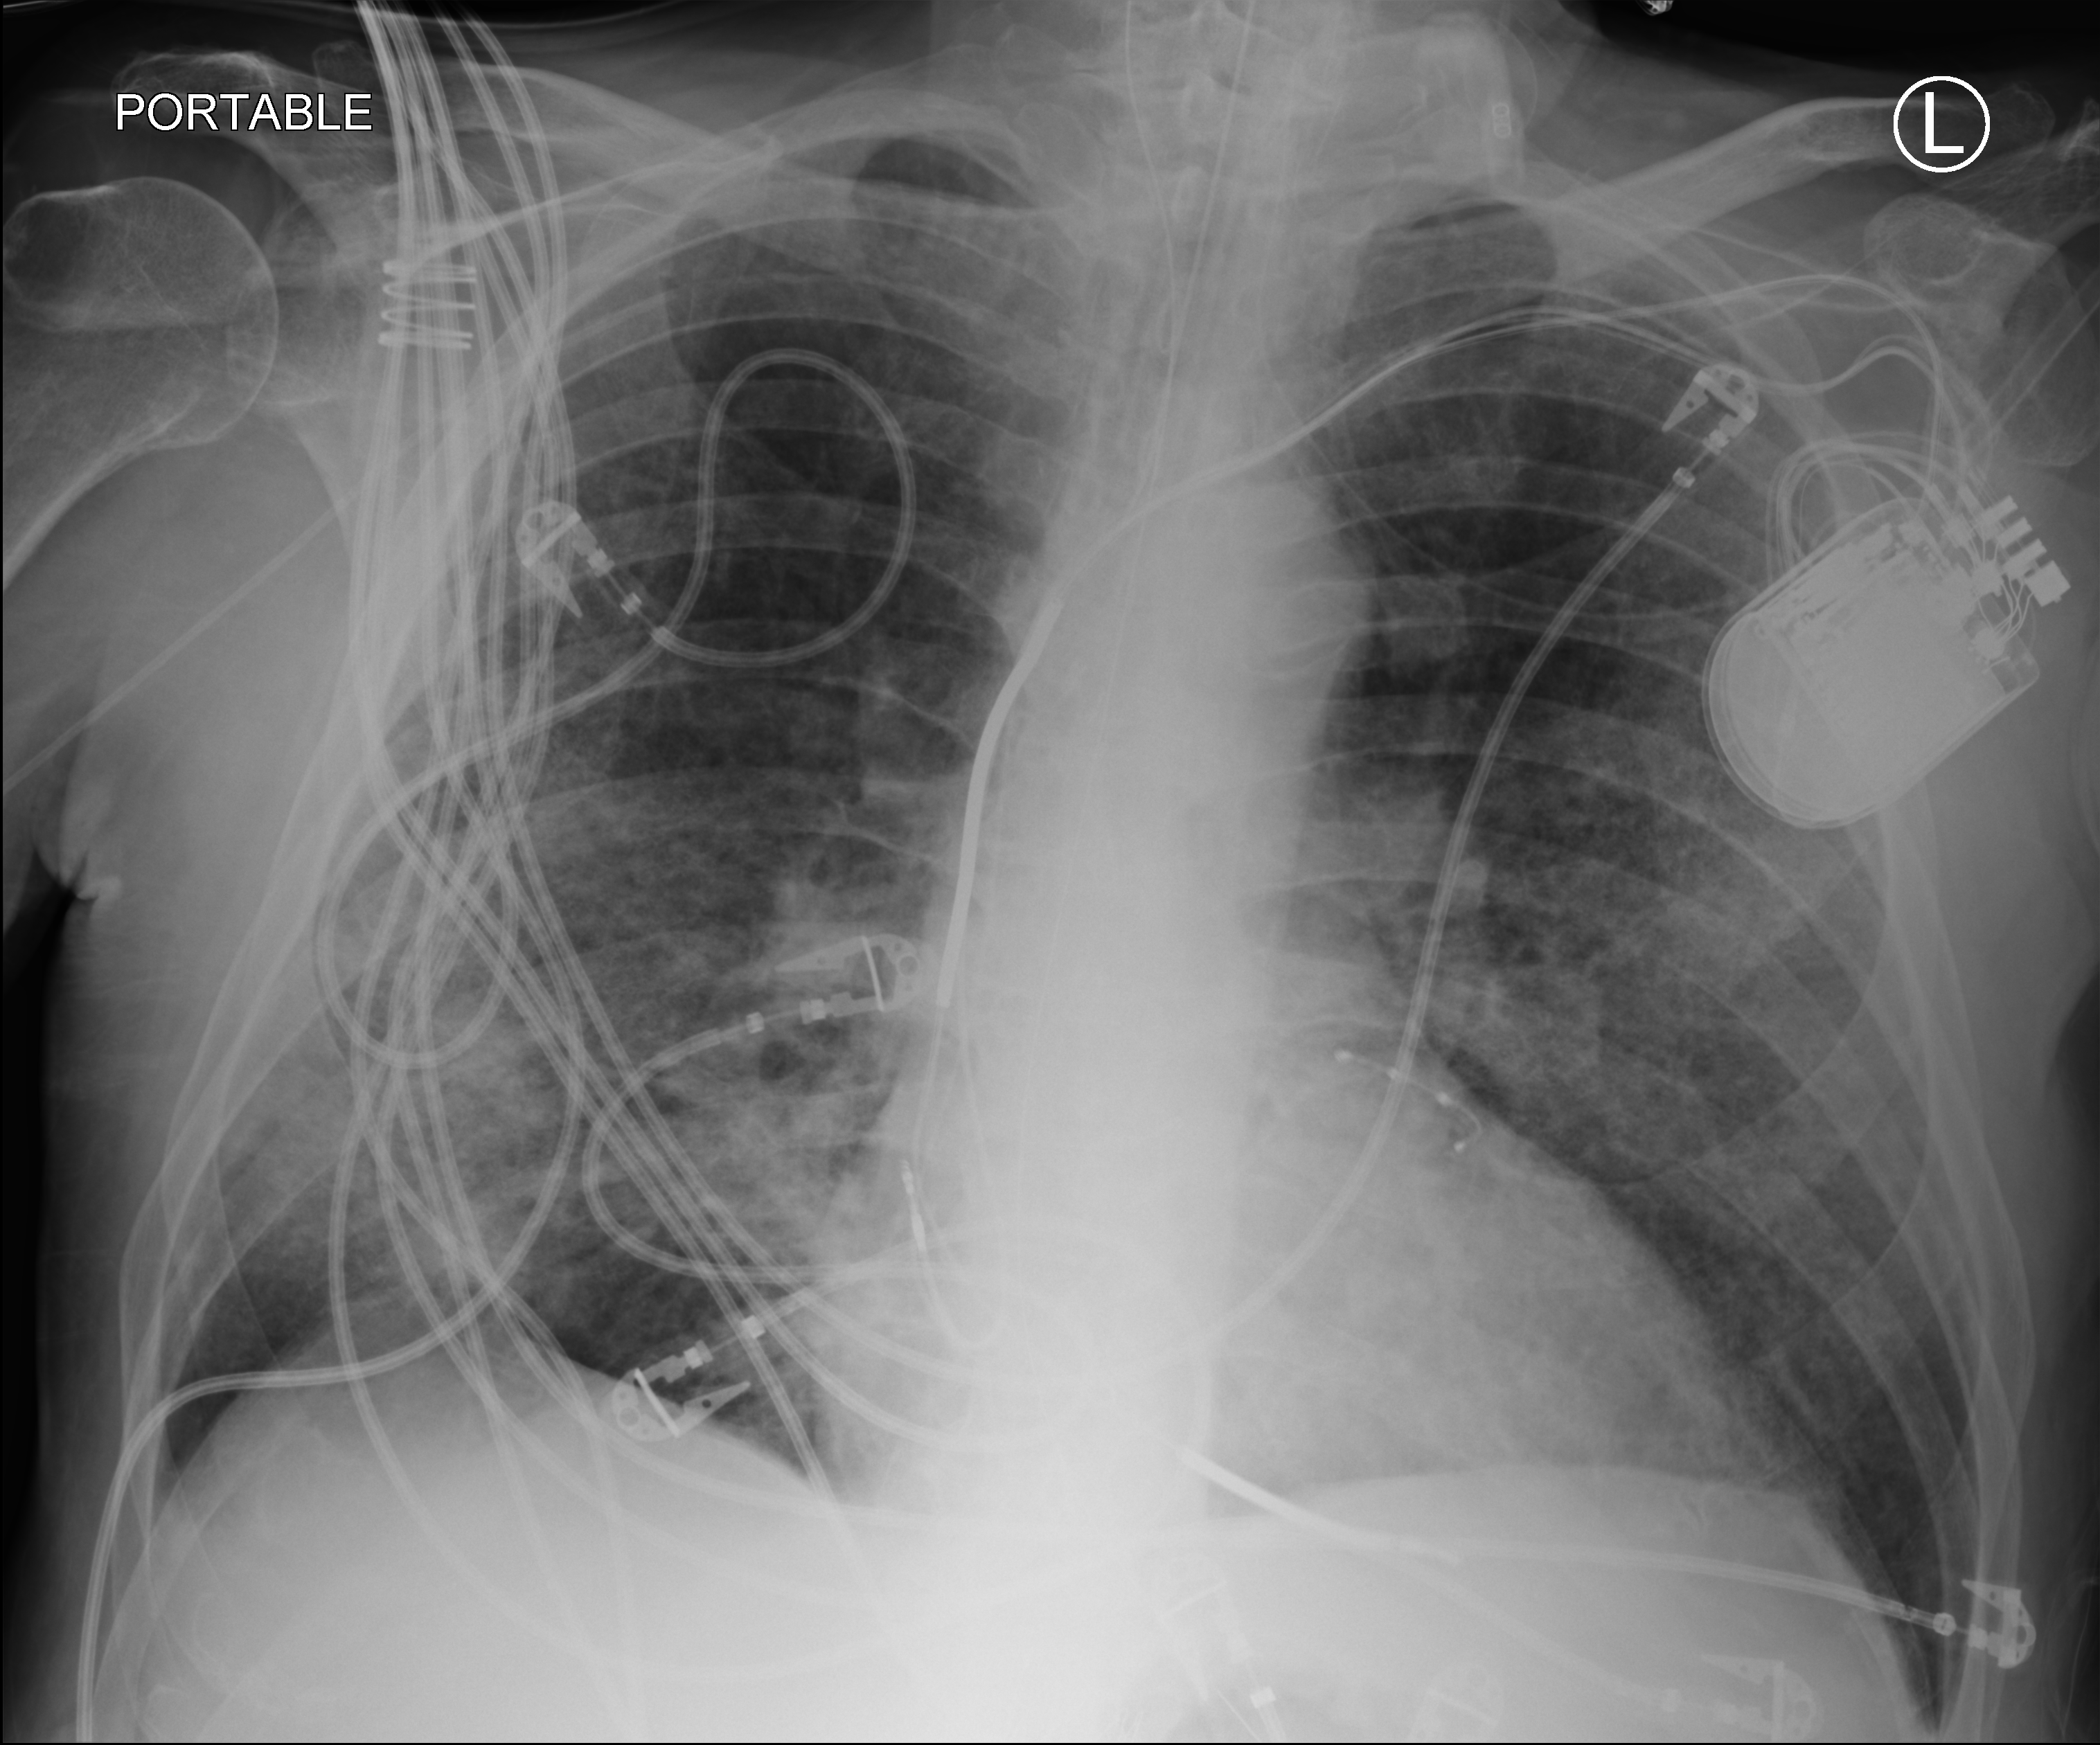
Chest X-ray (portable); anteroposterior (AP) projection. Patient hospitalised with COVID-19; male, aged 60–74 years.
Hospital-stay facts (about this admission, not read from this image; timing relative to this image not recorded): mechanically ventilated during this hospital stay: yes; length of hospital stay: 36 days; admitted to intensive care during this hospital stay: yes.